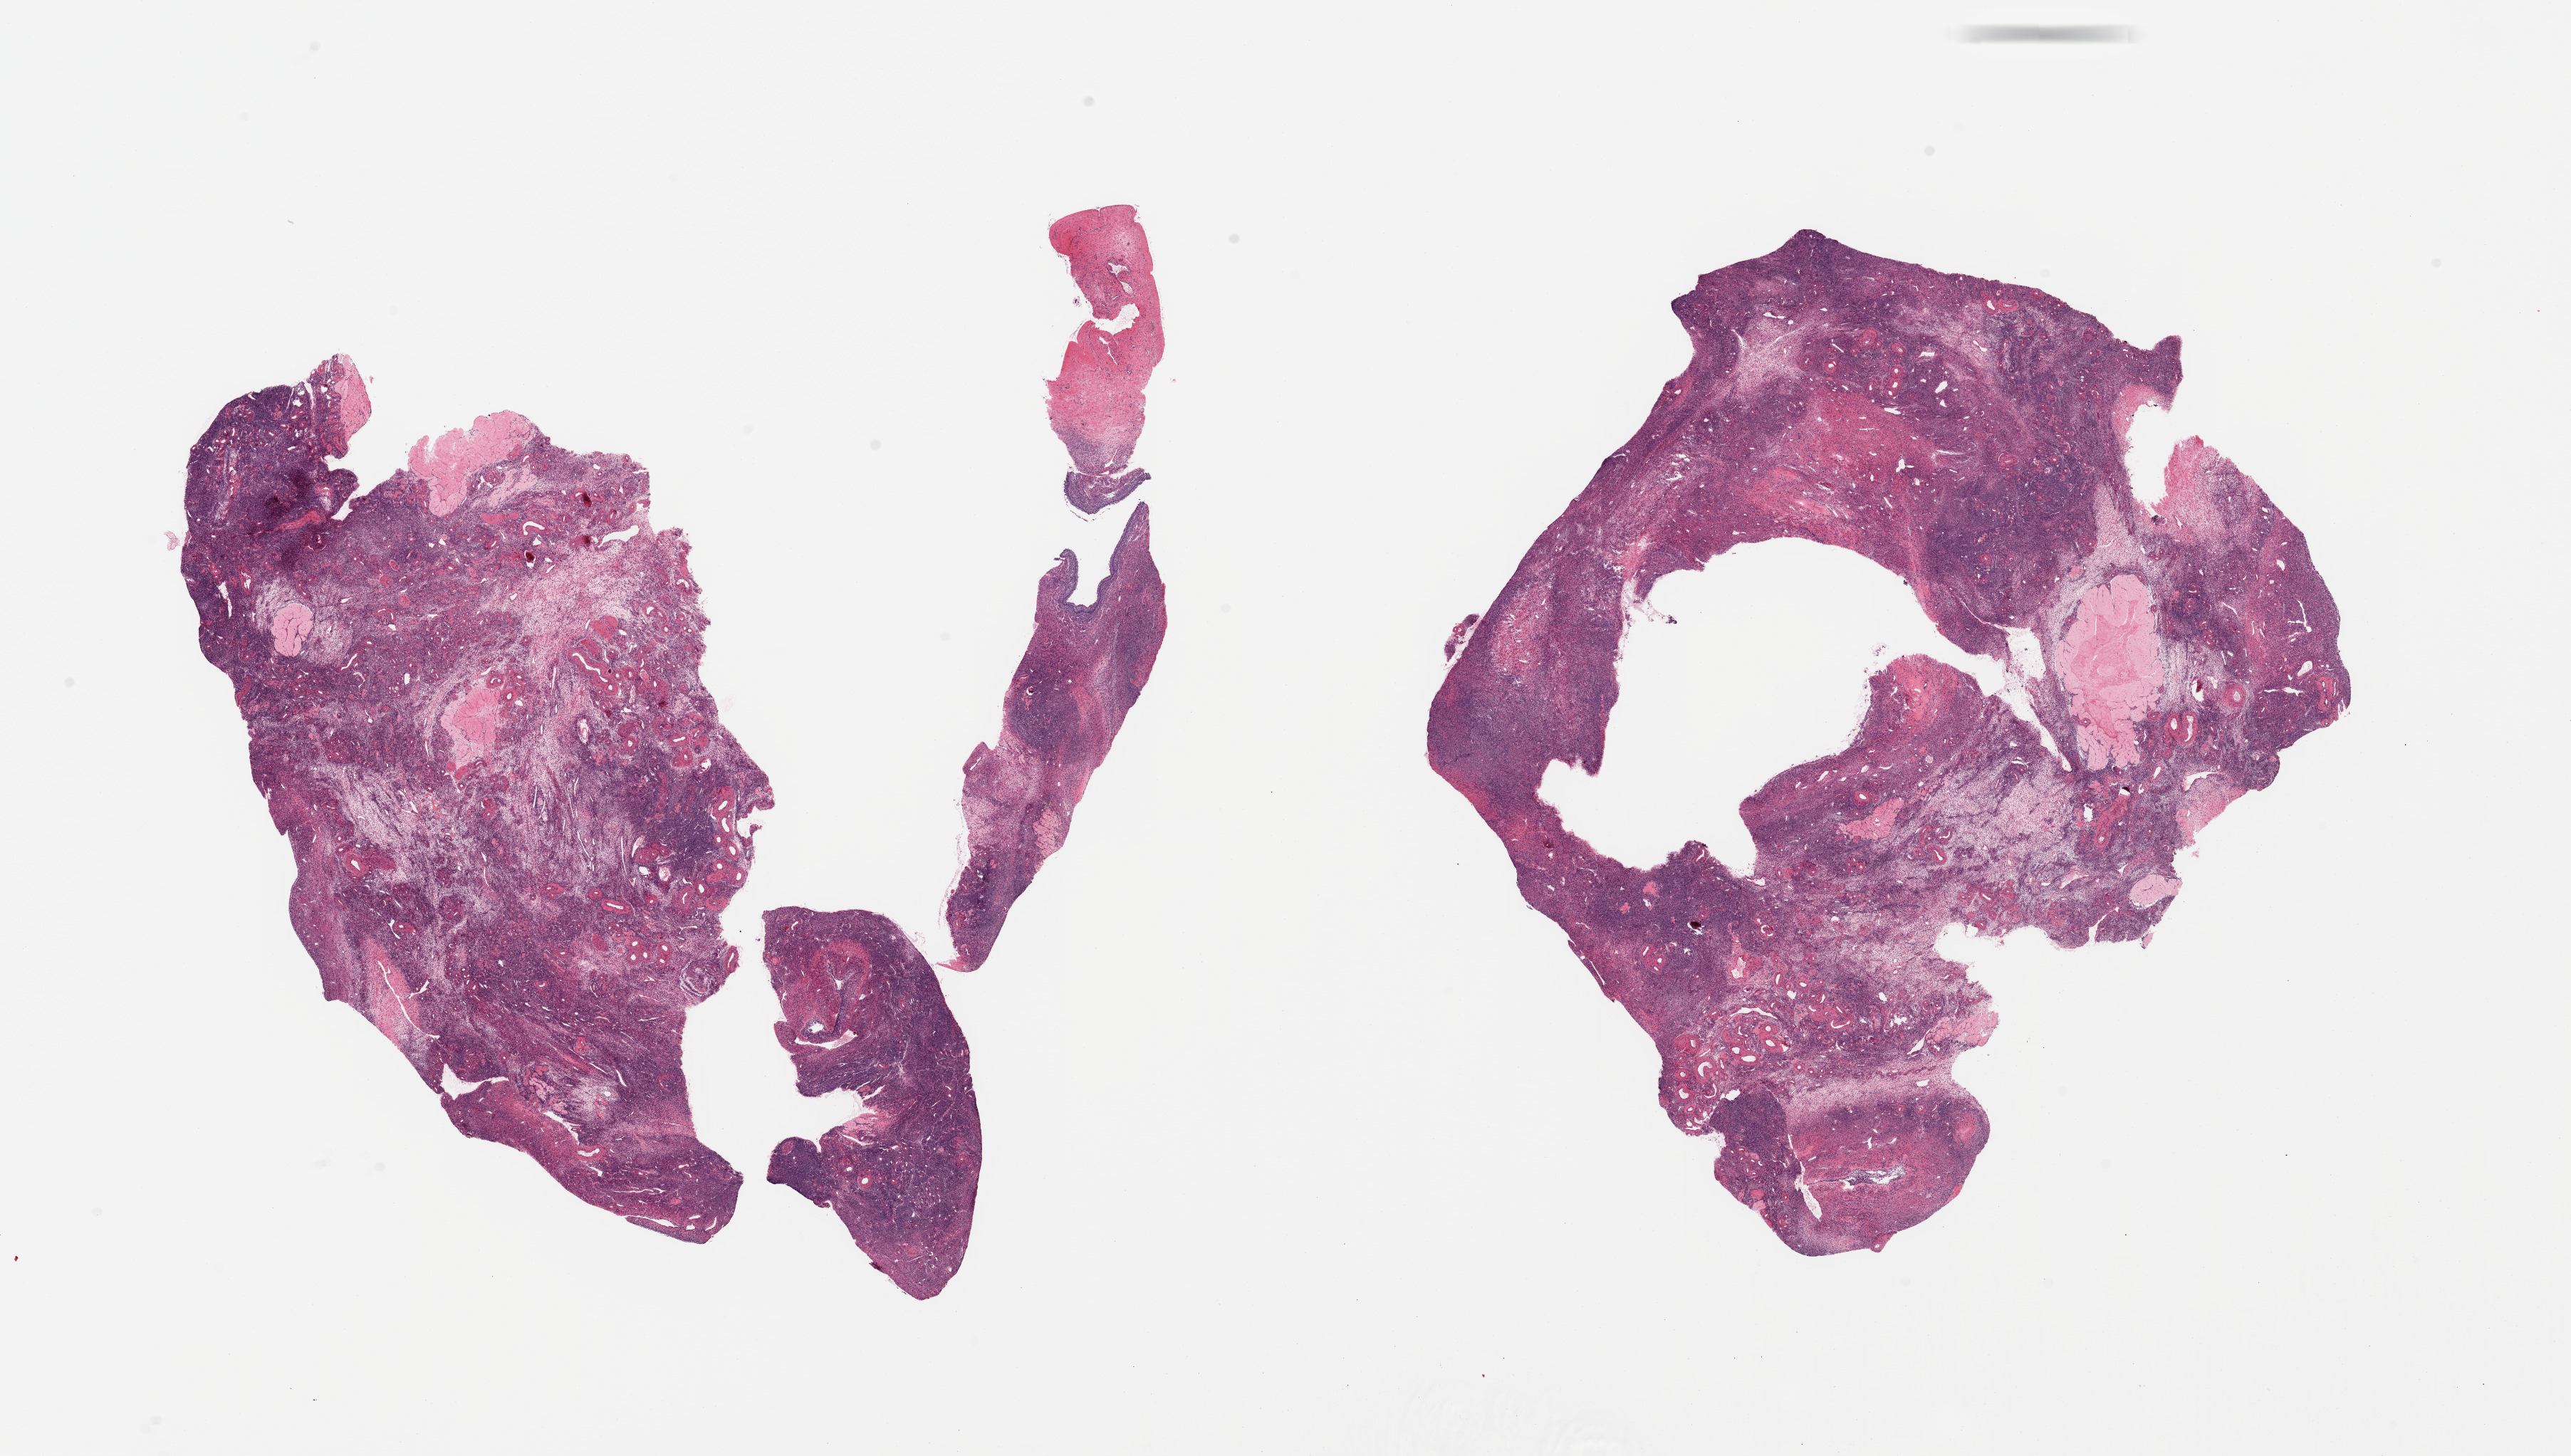
Hematoxylin and eosin (H&E) whole-slide image, brightfield, whole scanned area (about 28.5 x 16.2 mm, acquisition: 20x scan) shown as a low-resolution overview; PAXgene-fixed paraffin-embedded (PFPE) section; section of ovary (target tissue); donor tissue sample. Donor sex: female.
Pathologist's review note for this sample: 2 pieces, atrophic for stated age of patient.